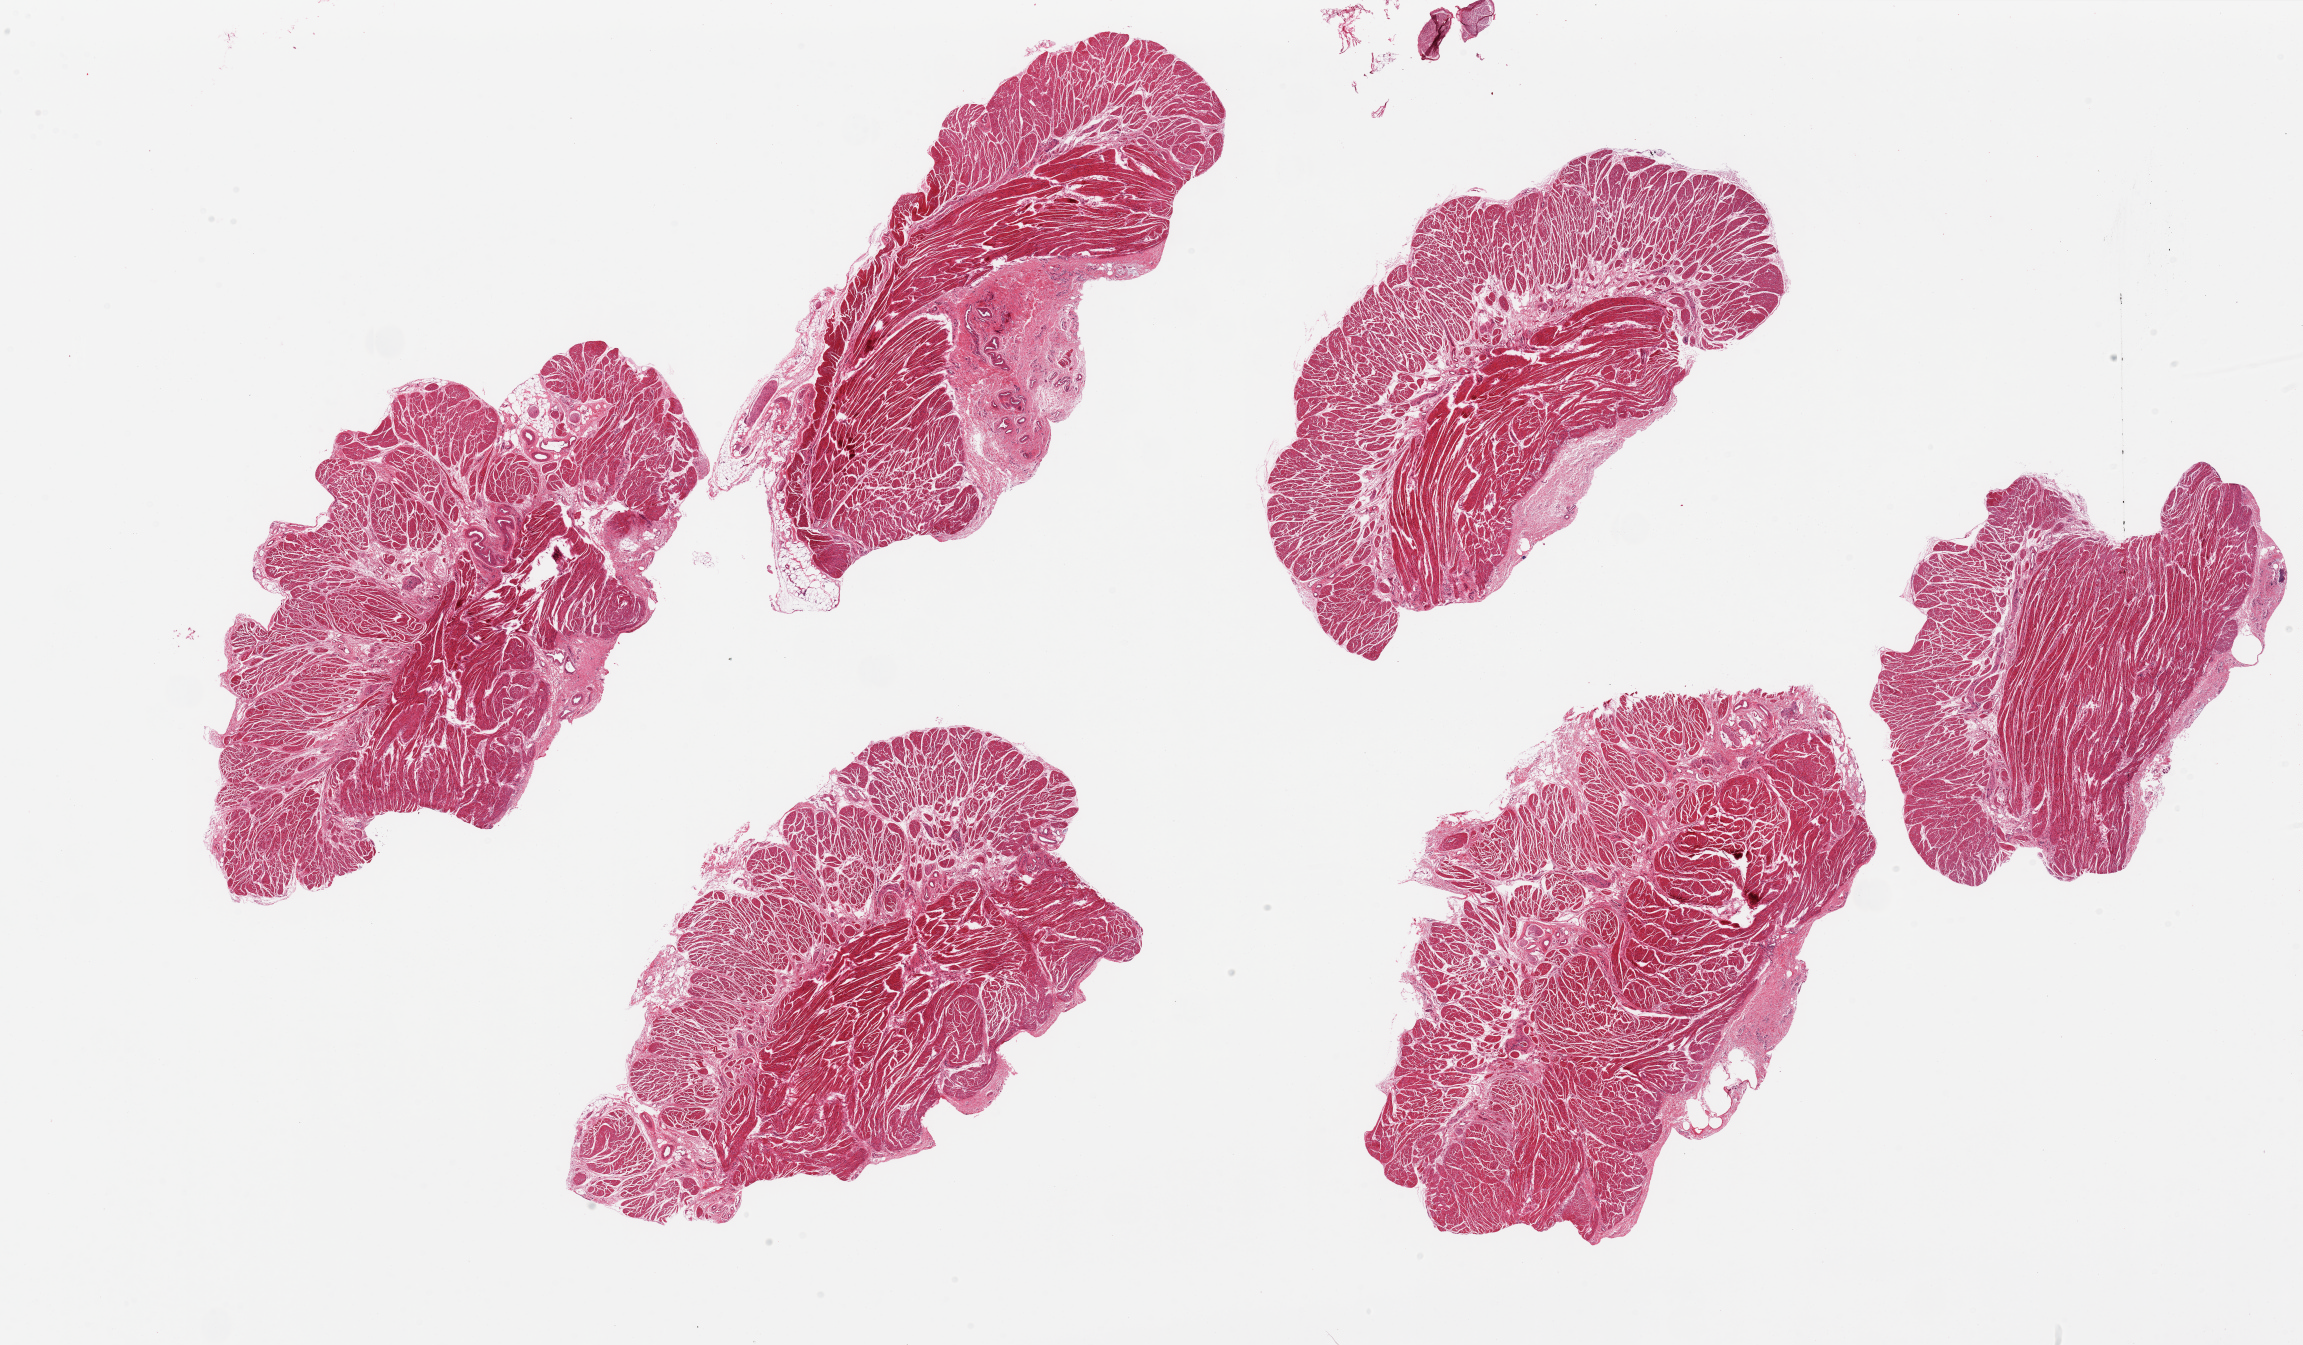
H&E whole-slide image — low-resolution overview of the scanned area, about 36.4 x 21.3 mm. PAXgene-fixed paraffin-embedded (PFPE) section. Section of esophageal muscle (target tissue). Donor tissue sample.
* review note (as recorded): 6 pieces, well trimmed, minute focus of squamous epithelium